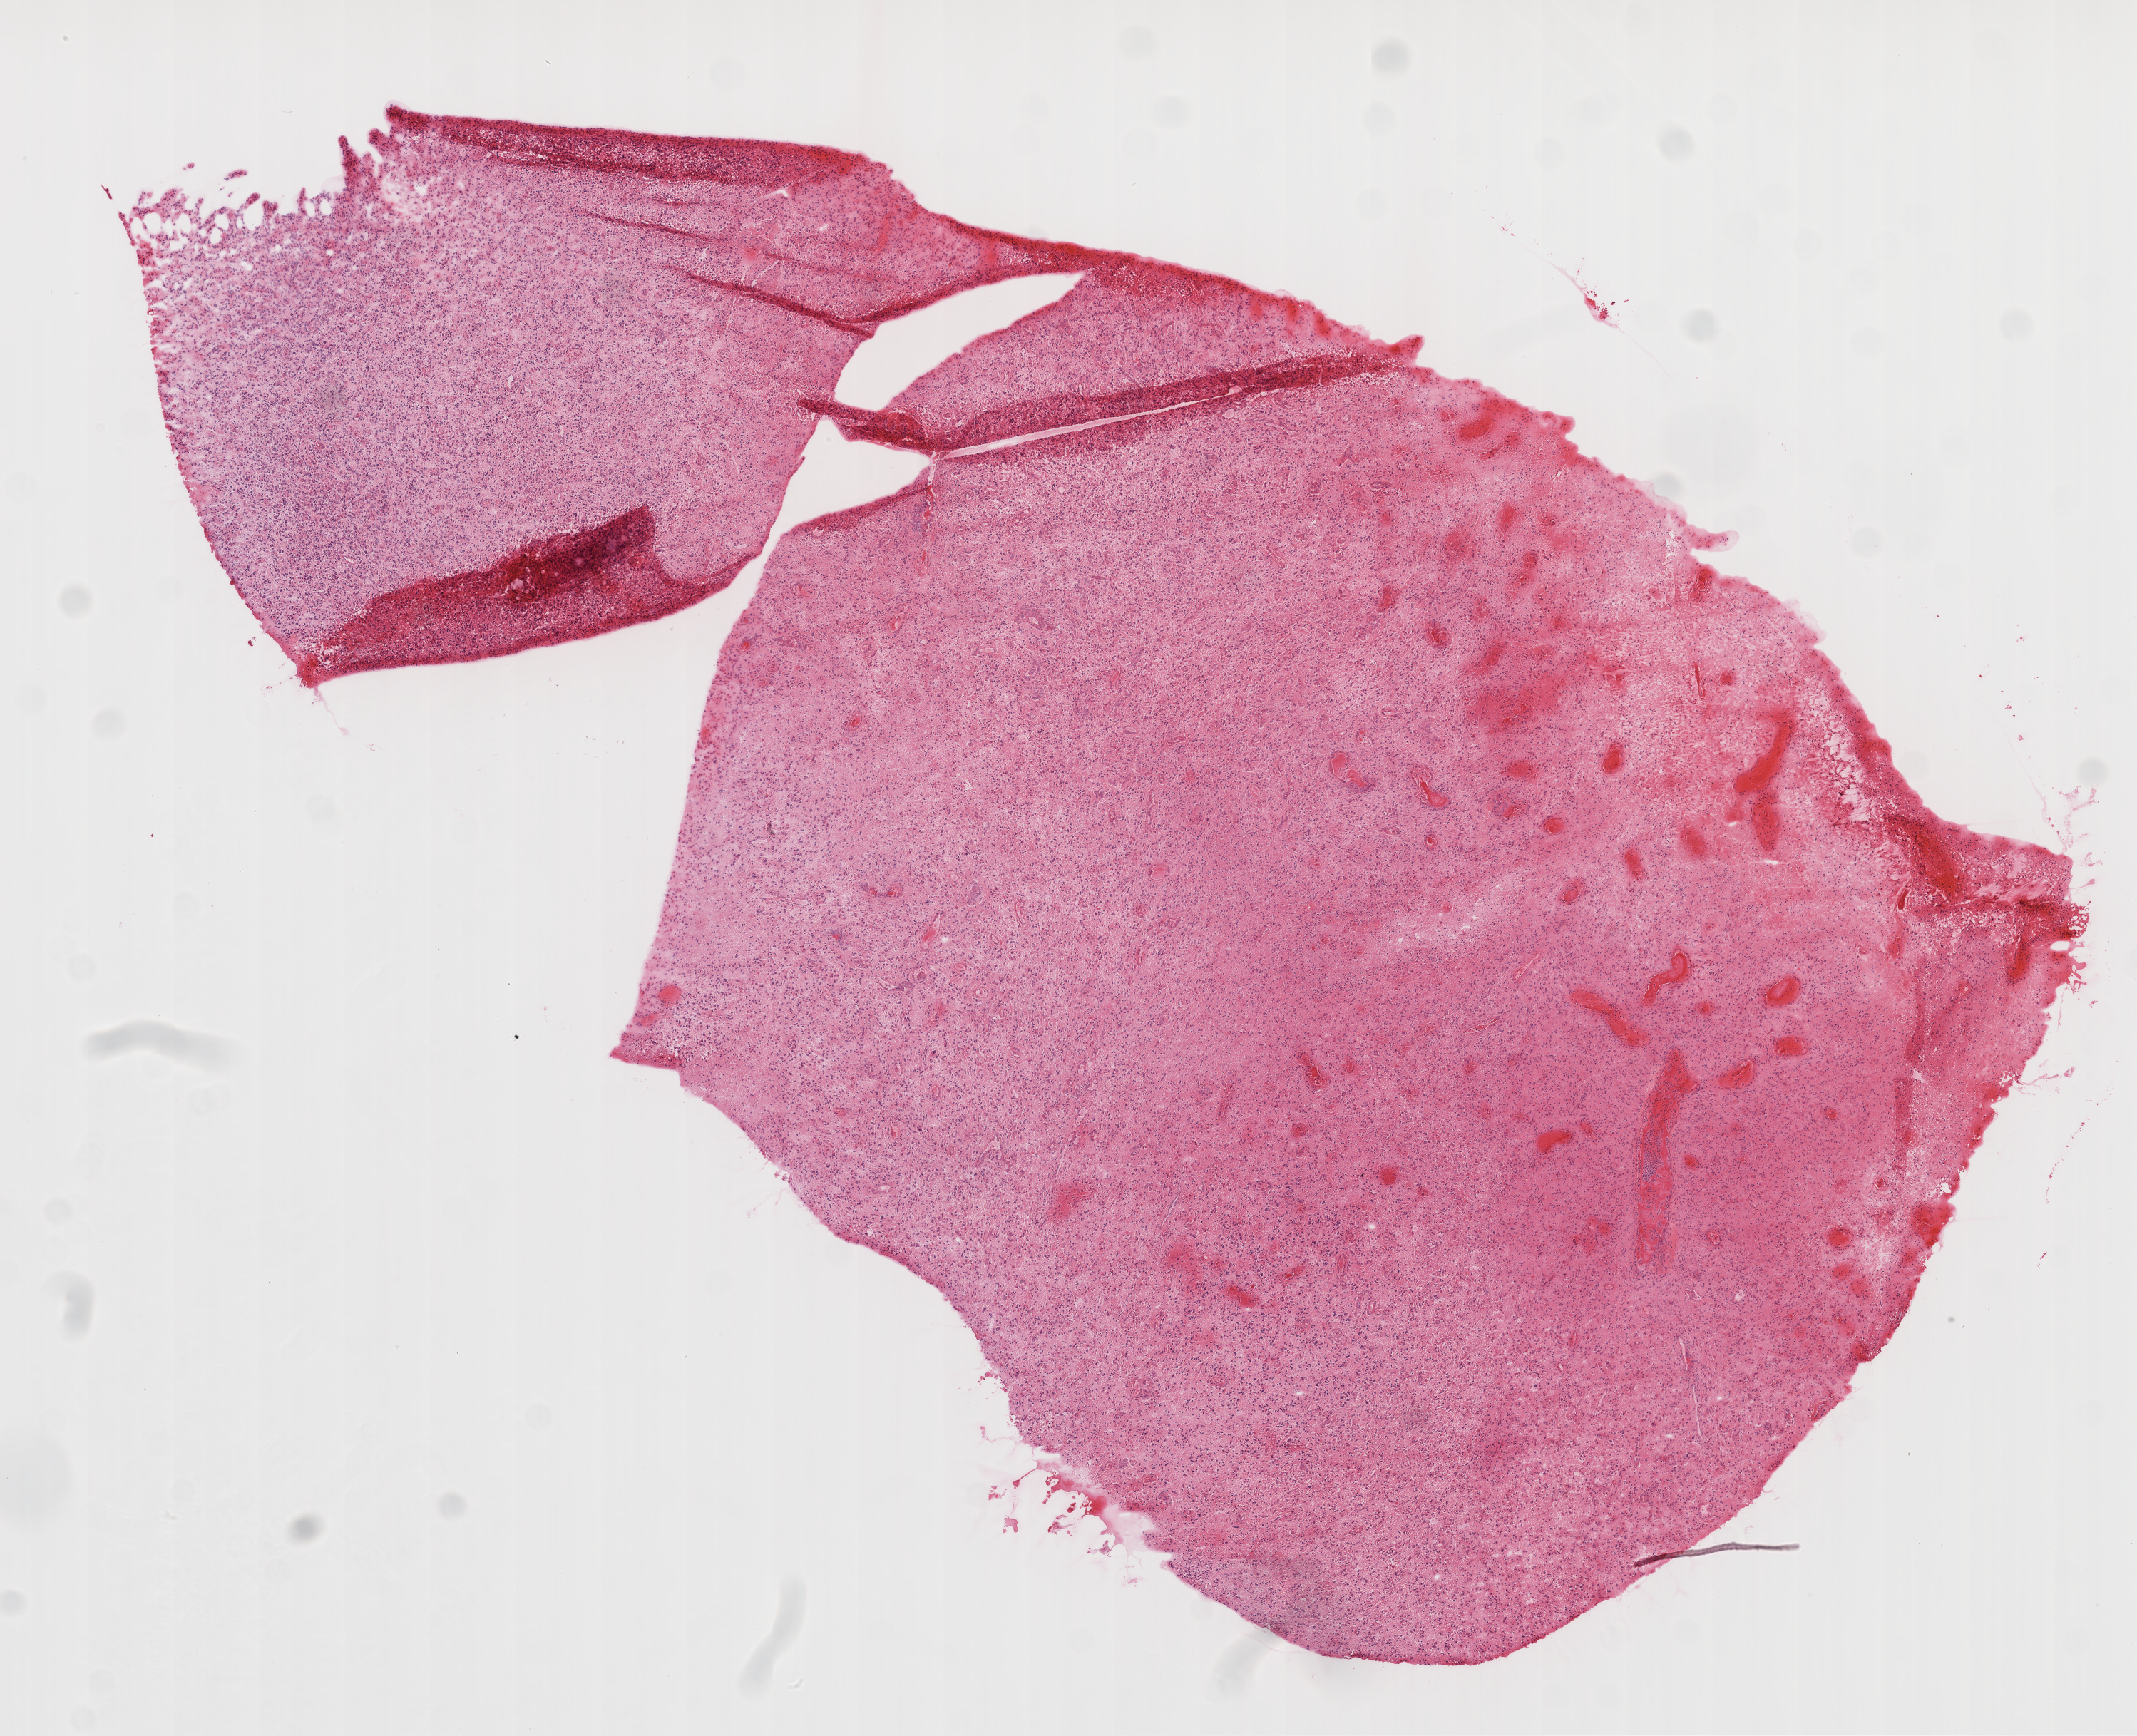
Digitized Hematoxylin and eosin (H&E) stained tissue section (whole slide), shown as a low-resolution overview of the whole scanned area (about 12.1 x 9.8 mm, acquisition: 20x scan), frozen section from the top of the tissue portion, sample: primary tumour, brain. Male, age 55 years at initial diagnosis. Composition of this section per pathologist review: tumour cells 80%, tumour nuclei 90%, normal cells 0%, stromal cells 0%, necrosis 20%. Infiltration values recorded for this section: neutrophil infiltration 100%.
* pathologic diagnosis: Glioblastoma